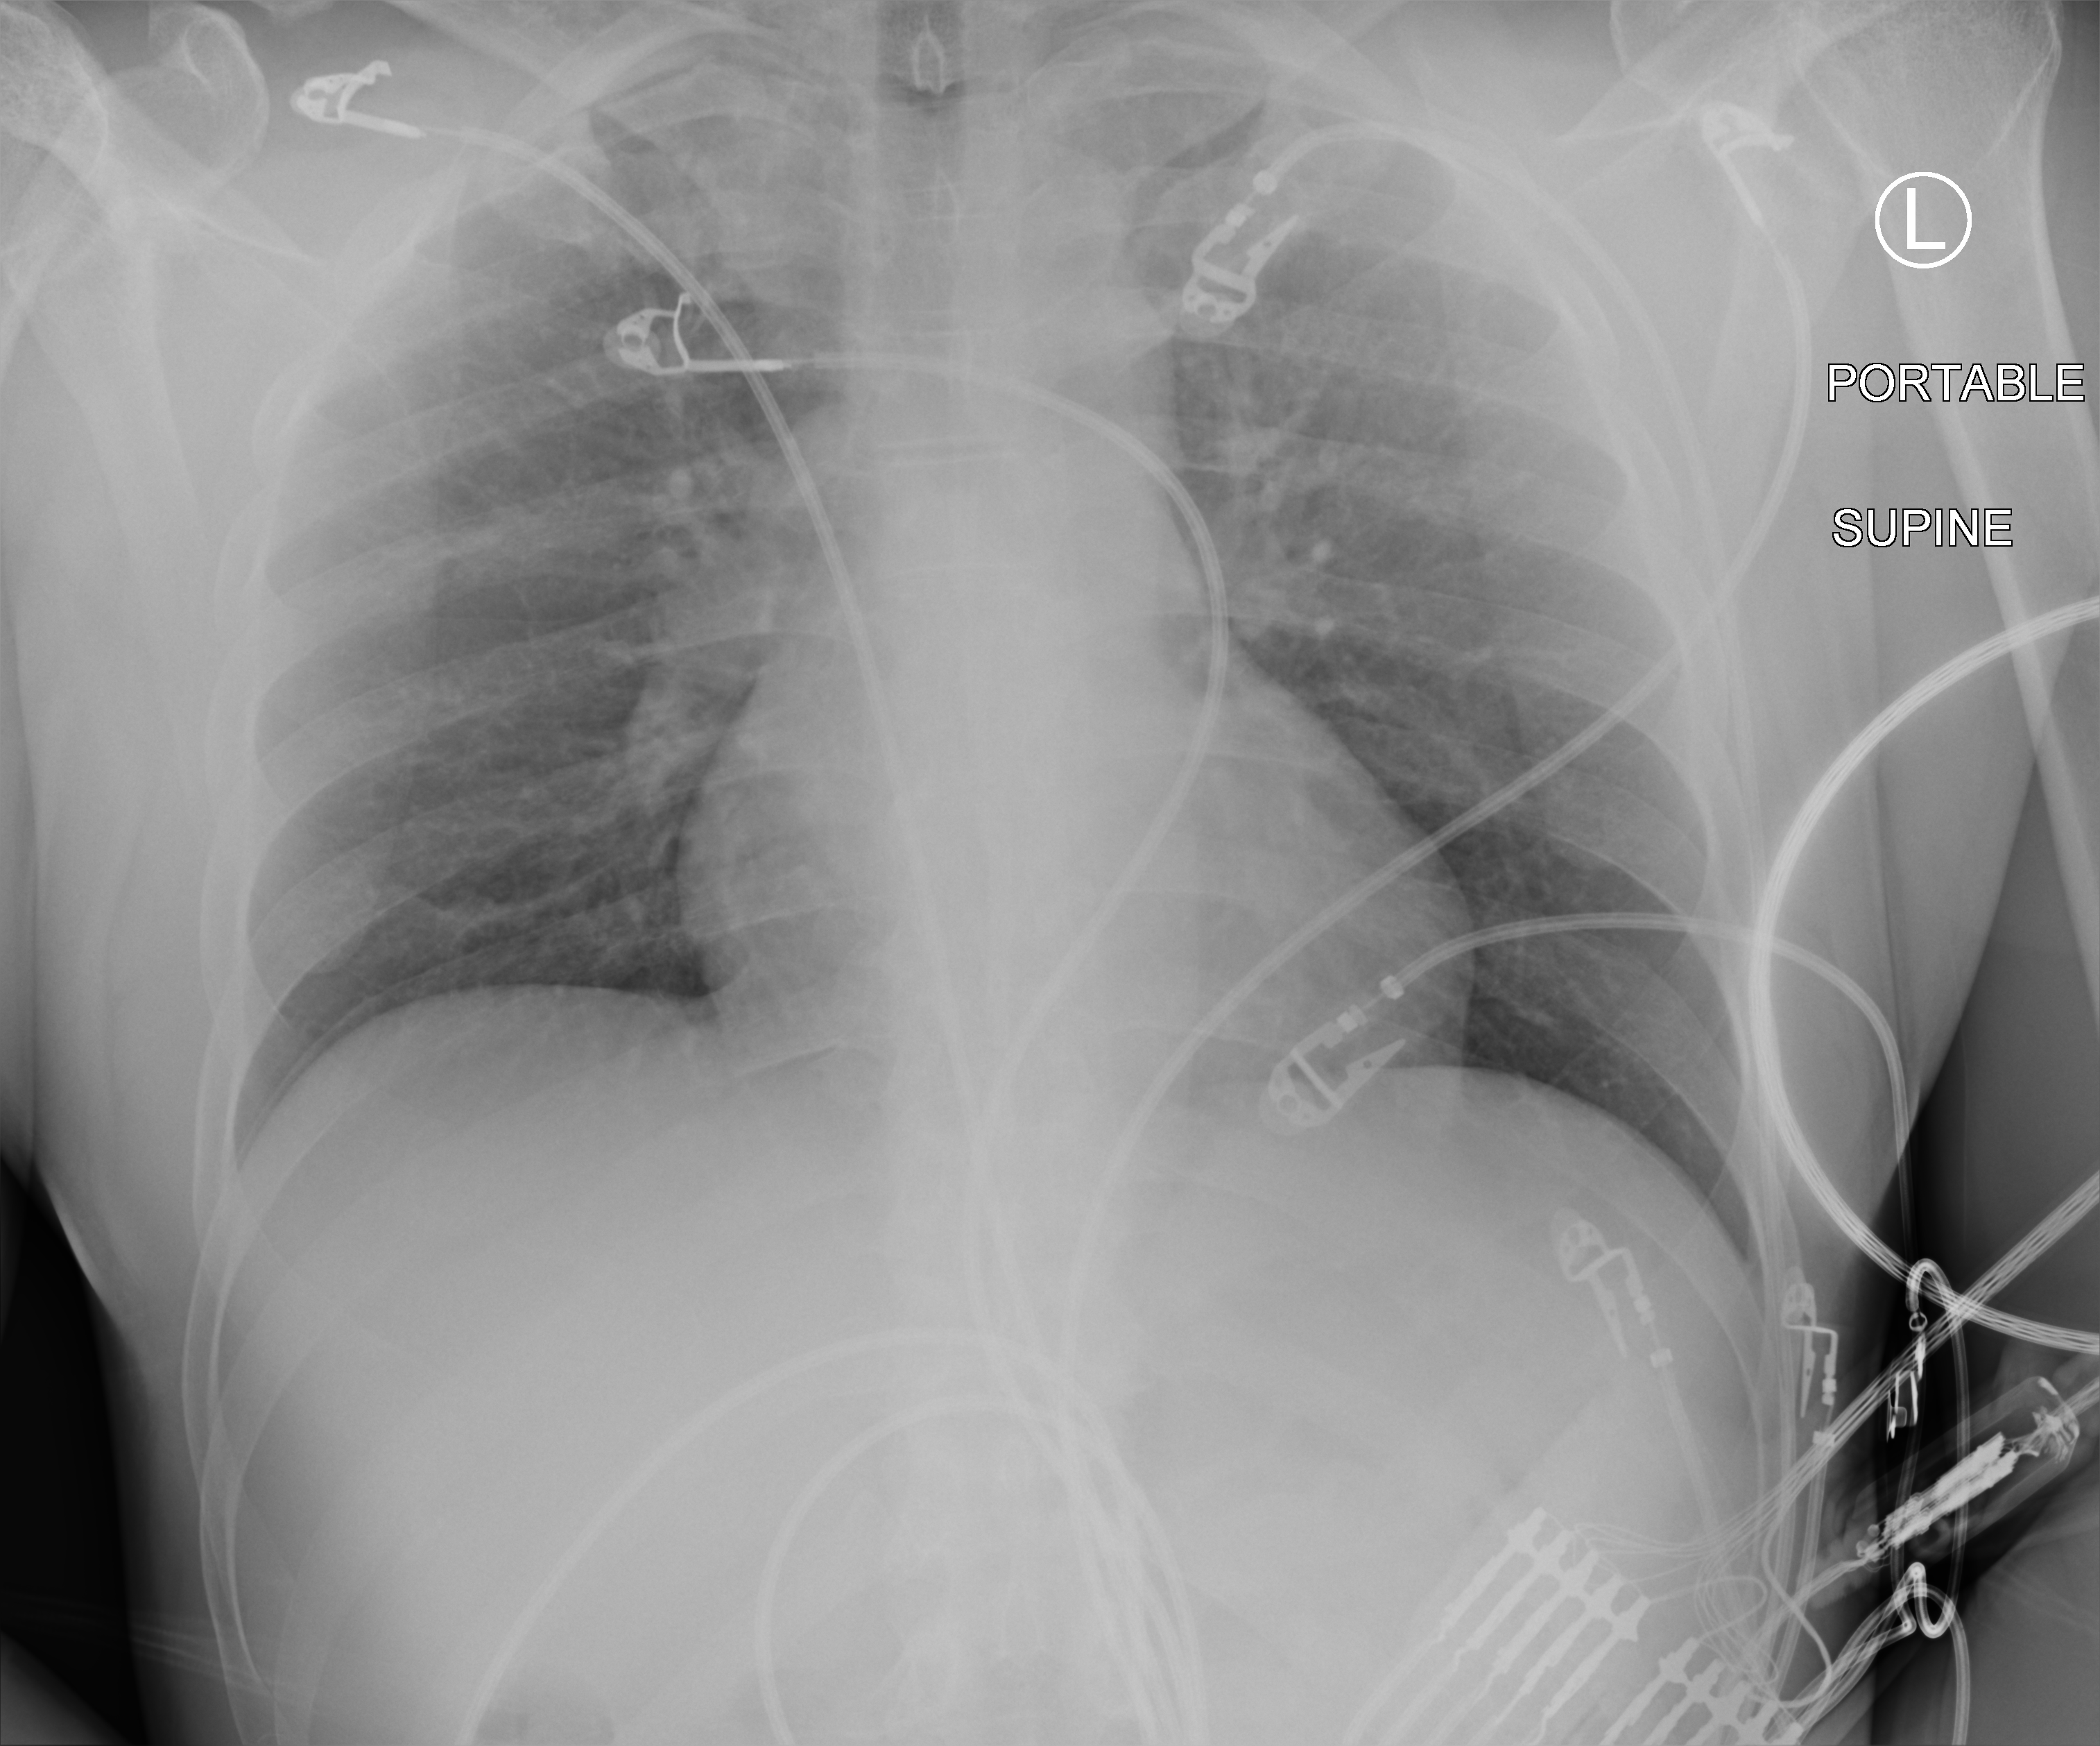
Bedside chest radiograph (computed radiography); anteroposterior (AP) projection. Patient hospitalised with COVID-19; male, aged 18–59 years.
Hospital-stay facts (about this admission, not read from this image; timing relative to this image not recorded): chronic kidney disease (admission record): no; hypertension (admission record): no.